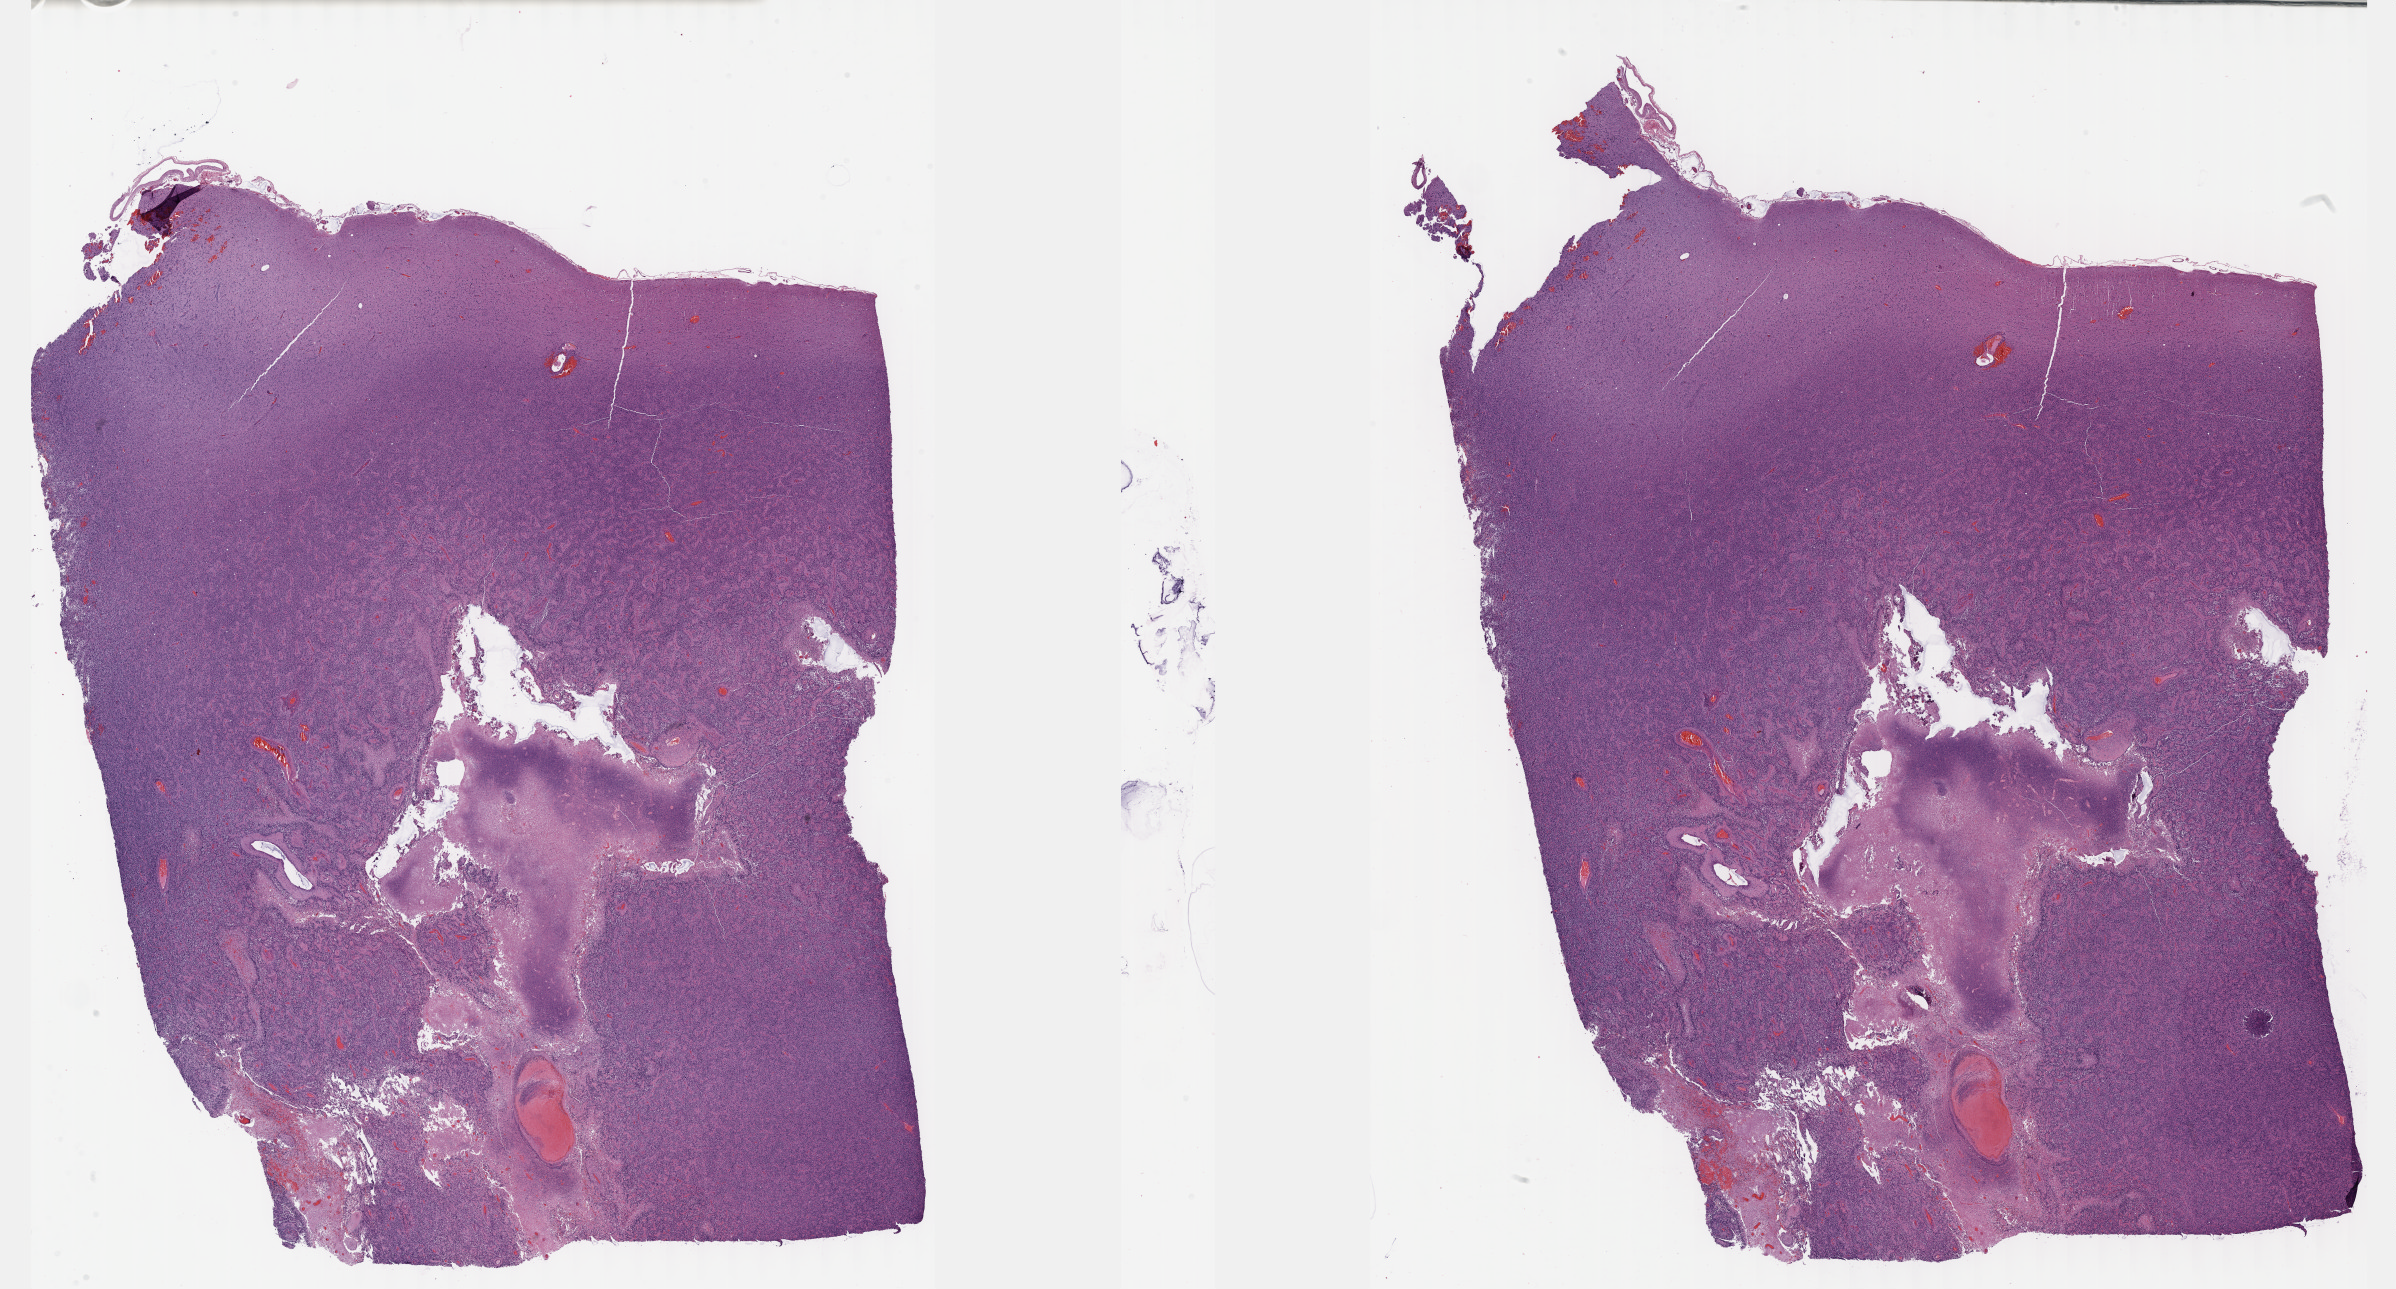
Digitized H&E-stained tissue section (whole slide) — whole scanned area (about 38.7 x 20.8 mm, acquisition: 40x scan) shown as a low-resolution overview; formalin-fixed paraffin-embedded (FFPE) diagnostic section; sample: primary tumour, brain. Male patient; age at initial diagnosis 40 years.
- pathologic diagnosis: Glioblastoma